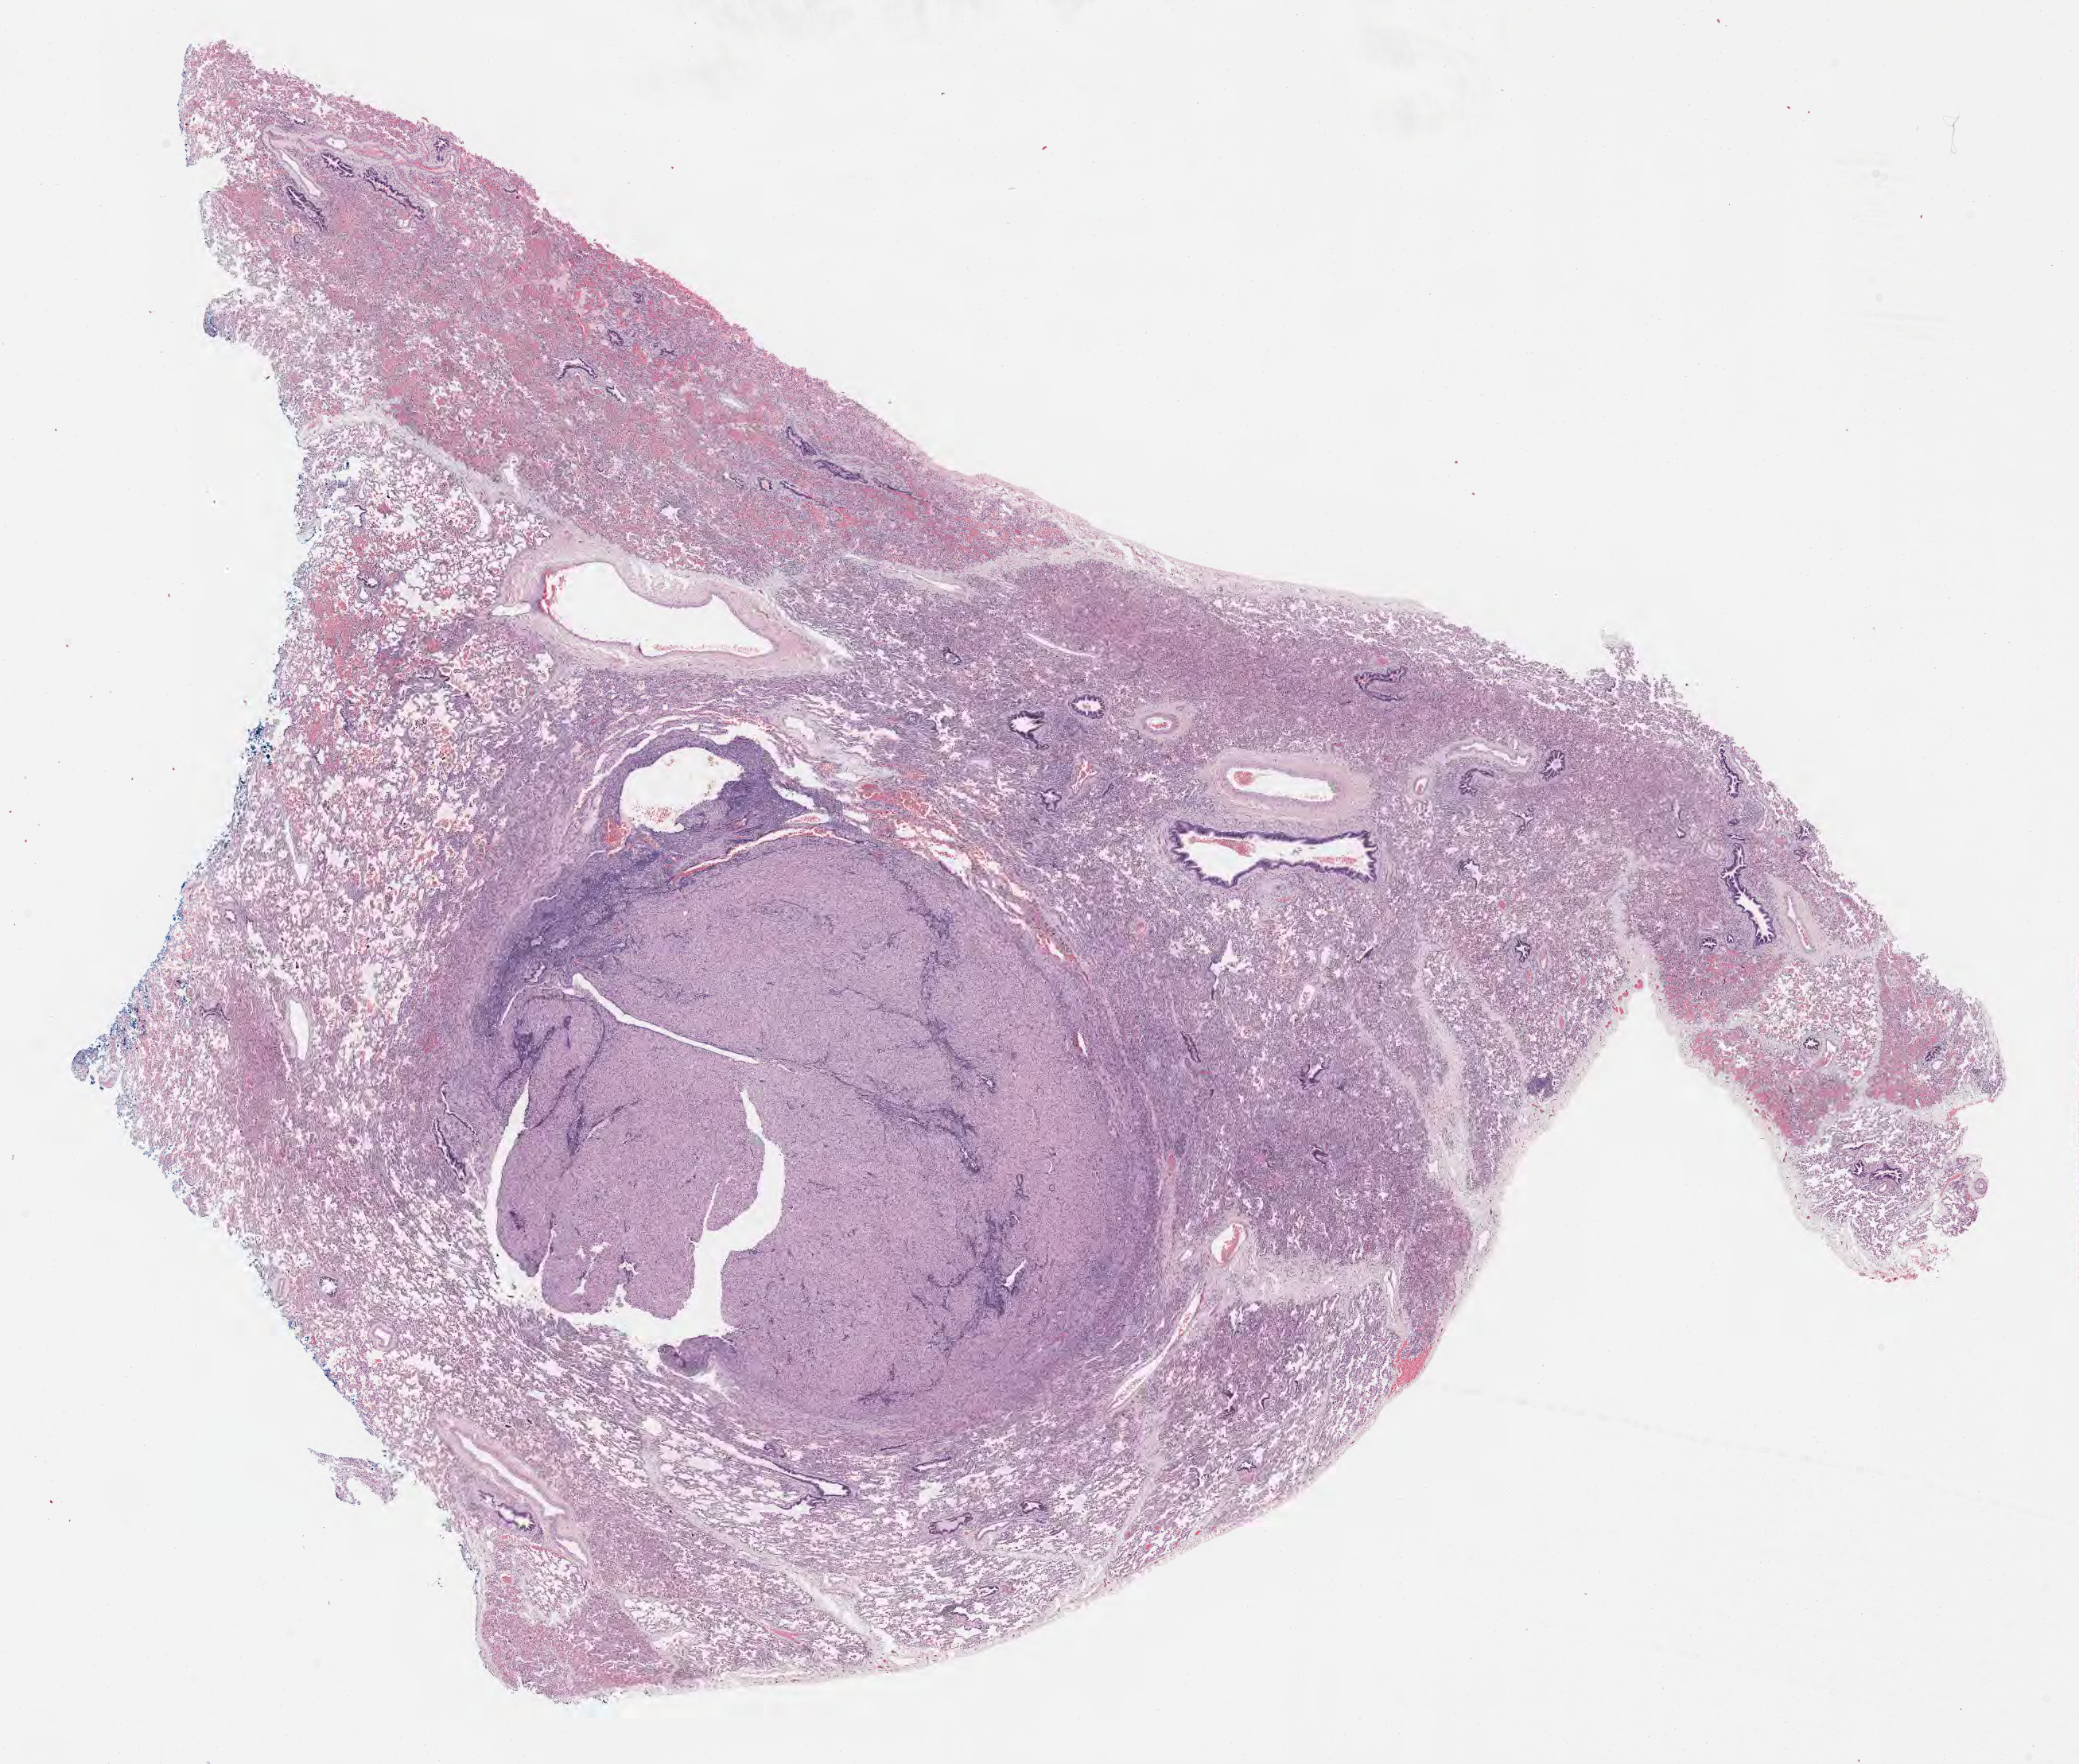
Hematoxylin and eosin (H&E) whole-slide image — a low-resolution overview of the entire scanned area, about 21.1 x 17.9 mm. FFPE section. Metastatic tumor tissue, resected from lung. Male patient; age at initial diagnosis 2 years. Composition of this section per pathologist review: tumor cells 25%, tumor nuclei 45%, stromal cells 10%, necrosis 0%, normal cells 65%. Infiltration values recorded for this section: lymphocyte infiltration 8%, monocyte infiltration 2%, neutrophil infiltration 0%.
• patient diagnosis (primary): Nephroblastoma, NOS
• section: bottom of the tissue portion